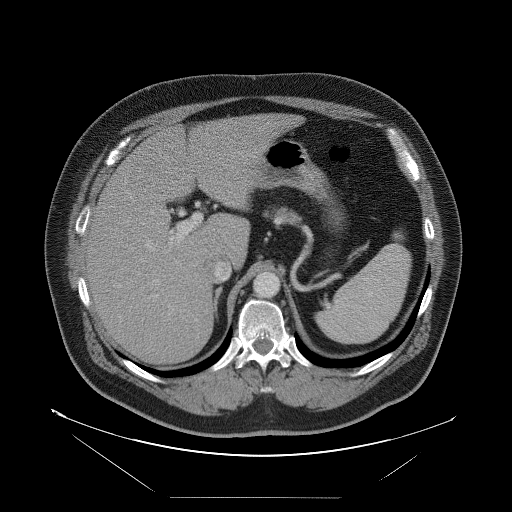
Contrast-enhanced abdominal CT, one axial slice. Position 64 of 114 along the scan axis. Intravenous contrast given. Soft-tissue window (W 400 / L 40 HU). 512 × 512 image matrix, field of view 500 × 500 mm. Male patient, age 61 years. Case-level facts recorded for this patient, not image findings: diagnosis: colorectal cancer liver metastases, imaged before liver resection; multiple liver metastases: no; largest metastasis: 6.5 cm; disease in both lobes: yes.
Structures marked on this image (expert manual segmentation):
- hepatic veins: bounding box (x1, y1, x2, y2) in pixels: (146, 241, 155, 250)
- liver: (88, 114, 290, 365)
- planned liver remnant (the part of the liver to remain after resection): (145, 114, 291, 258)
- portal vein (with intrahepatic branches): (152, 214, 202, 301)